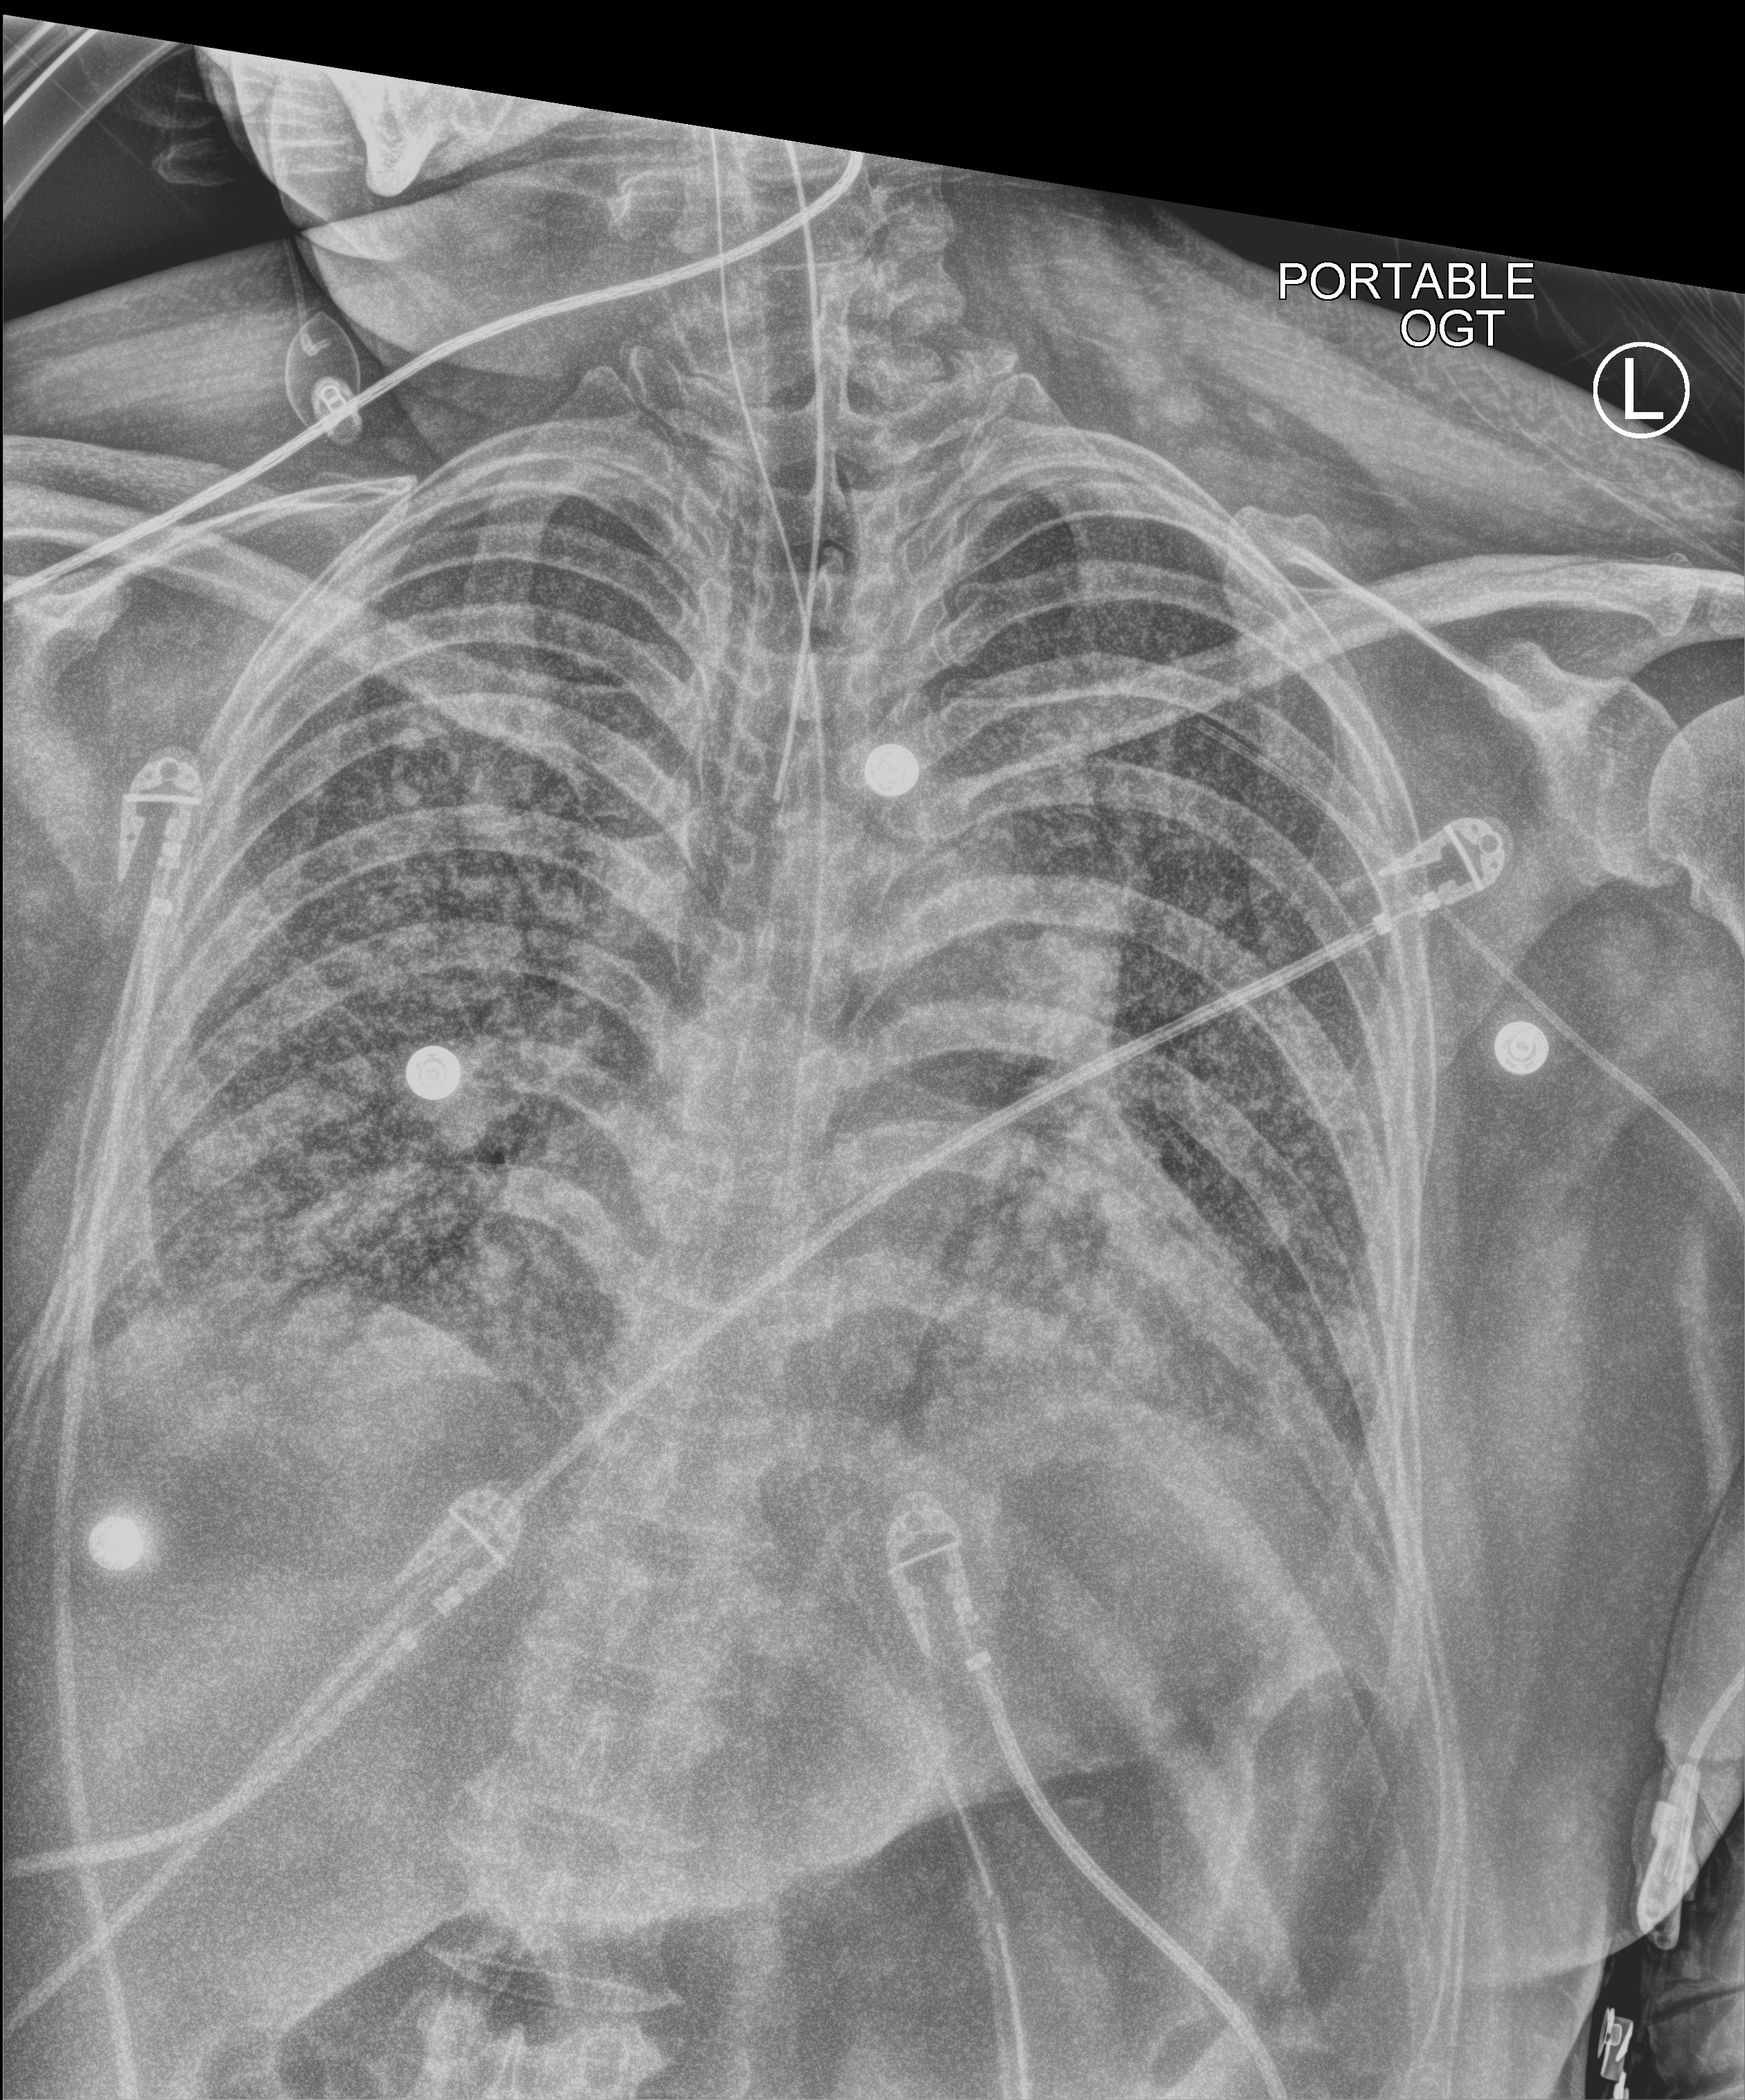
Portable chest radiograph, anteroposterior (AP) projection. Adult patient hospitalised with COVID-19, age 18–59 years.
Hospital-stay facts (about this admission, not read from this image; timing relative to this image not recorded):
- admitted to intensive care during this hospital stay: yes
- mechanically ventilated during this hospital stay: yes